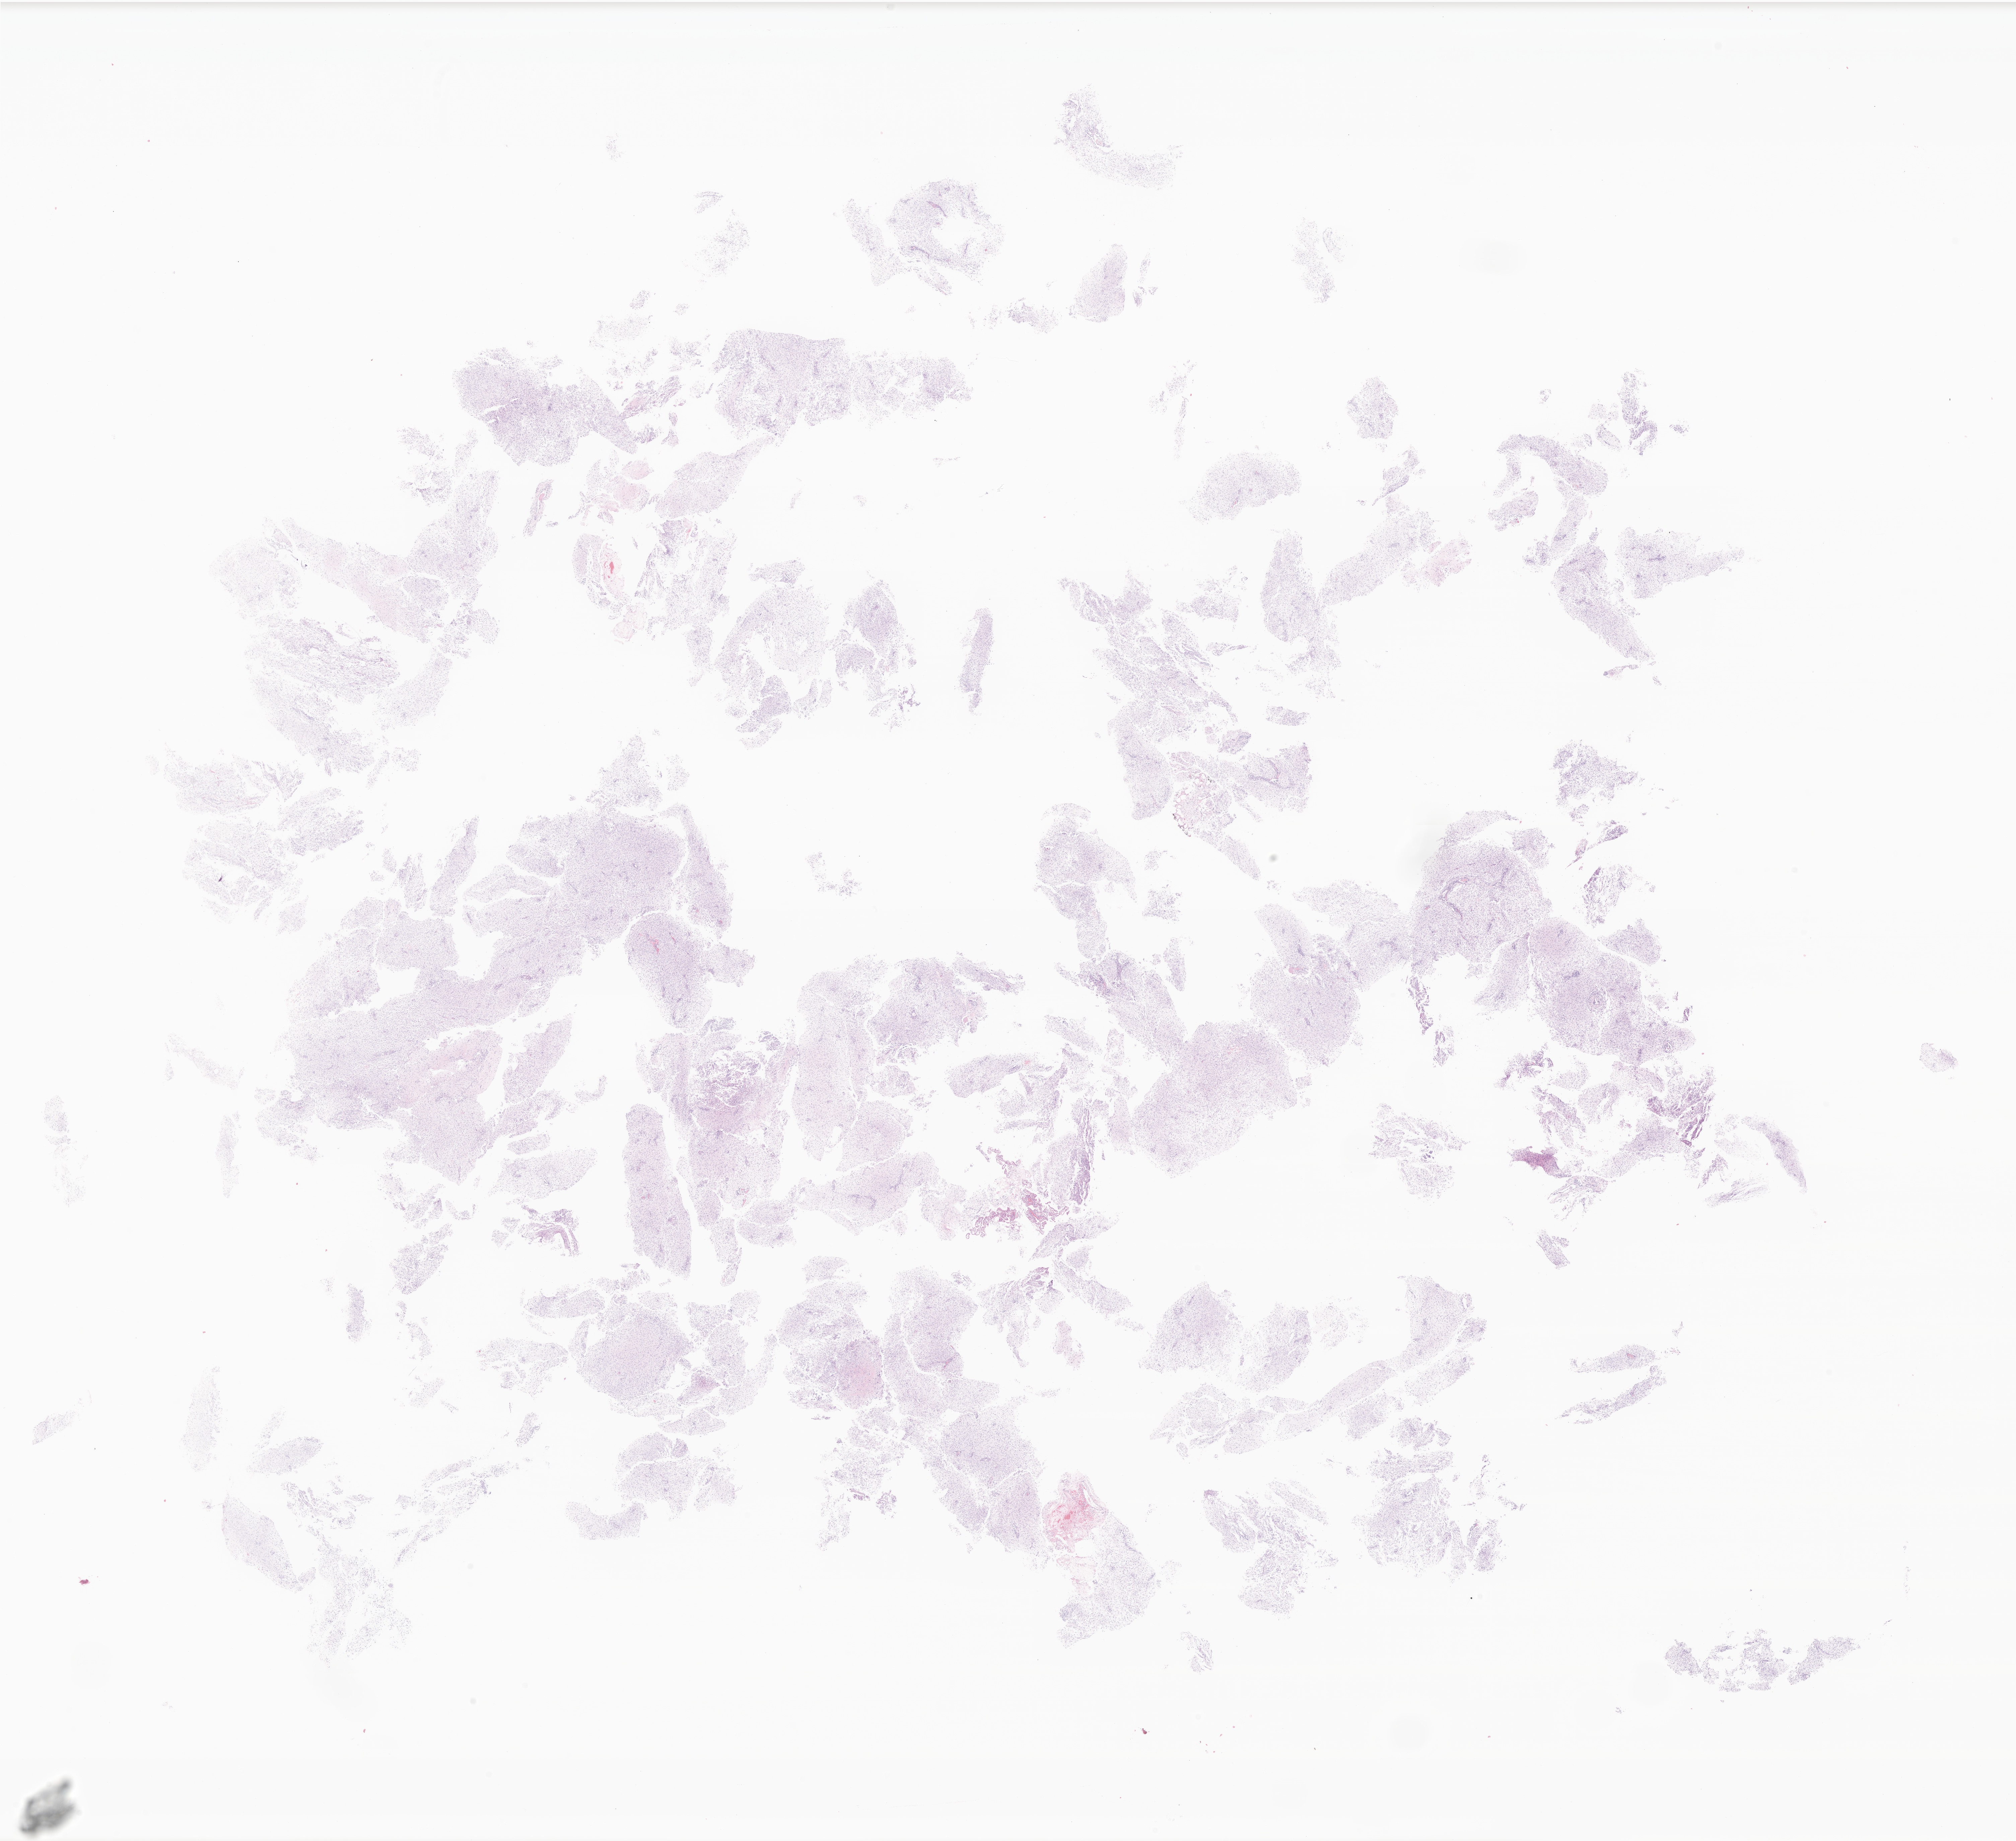
Whole-slide image, hematoxylin and eosin (H&E) stain of tumor tissue from the brain, shown as a low-resolution overview of the whole scanned area (about 25.4 x 23.2 mm). Formalin-fixed, paraffin-embedded (FFPE) tissue. Male patient, age 36 months (3 years).
* diagnosis (ICD-O-3 morphology term): Glioma, malignant